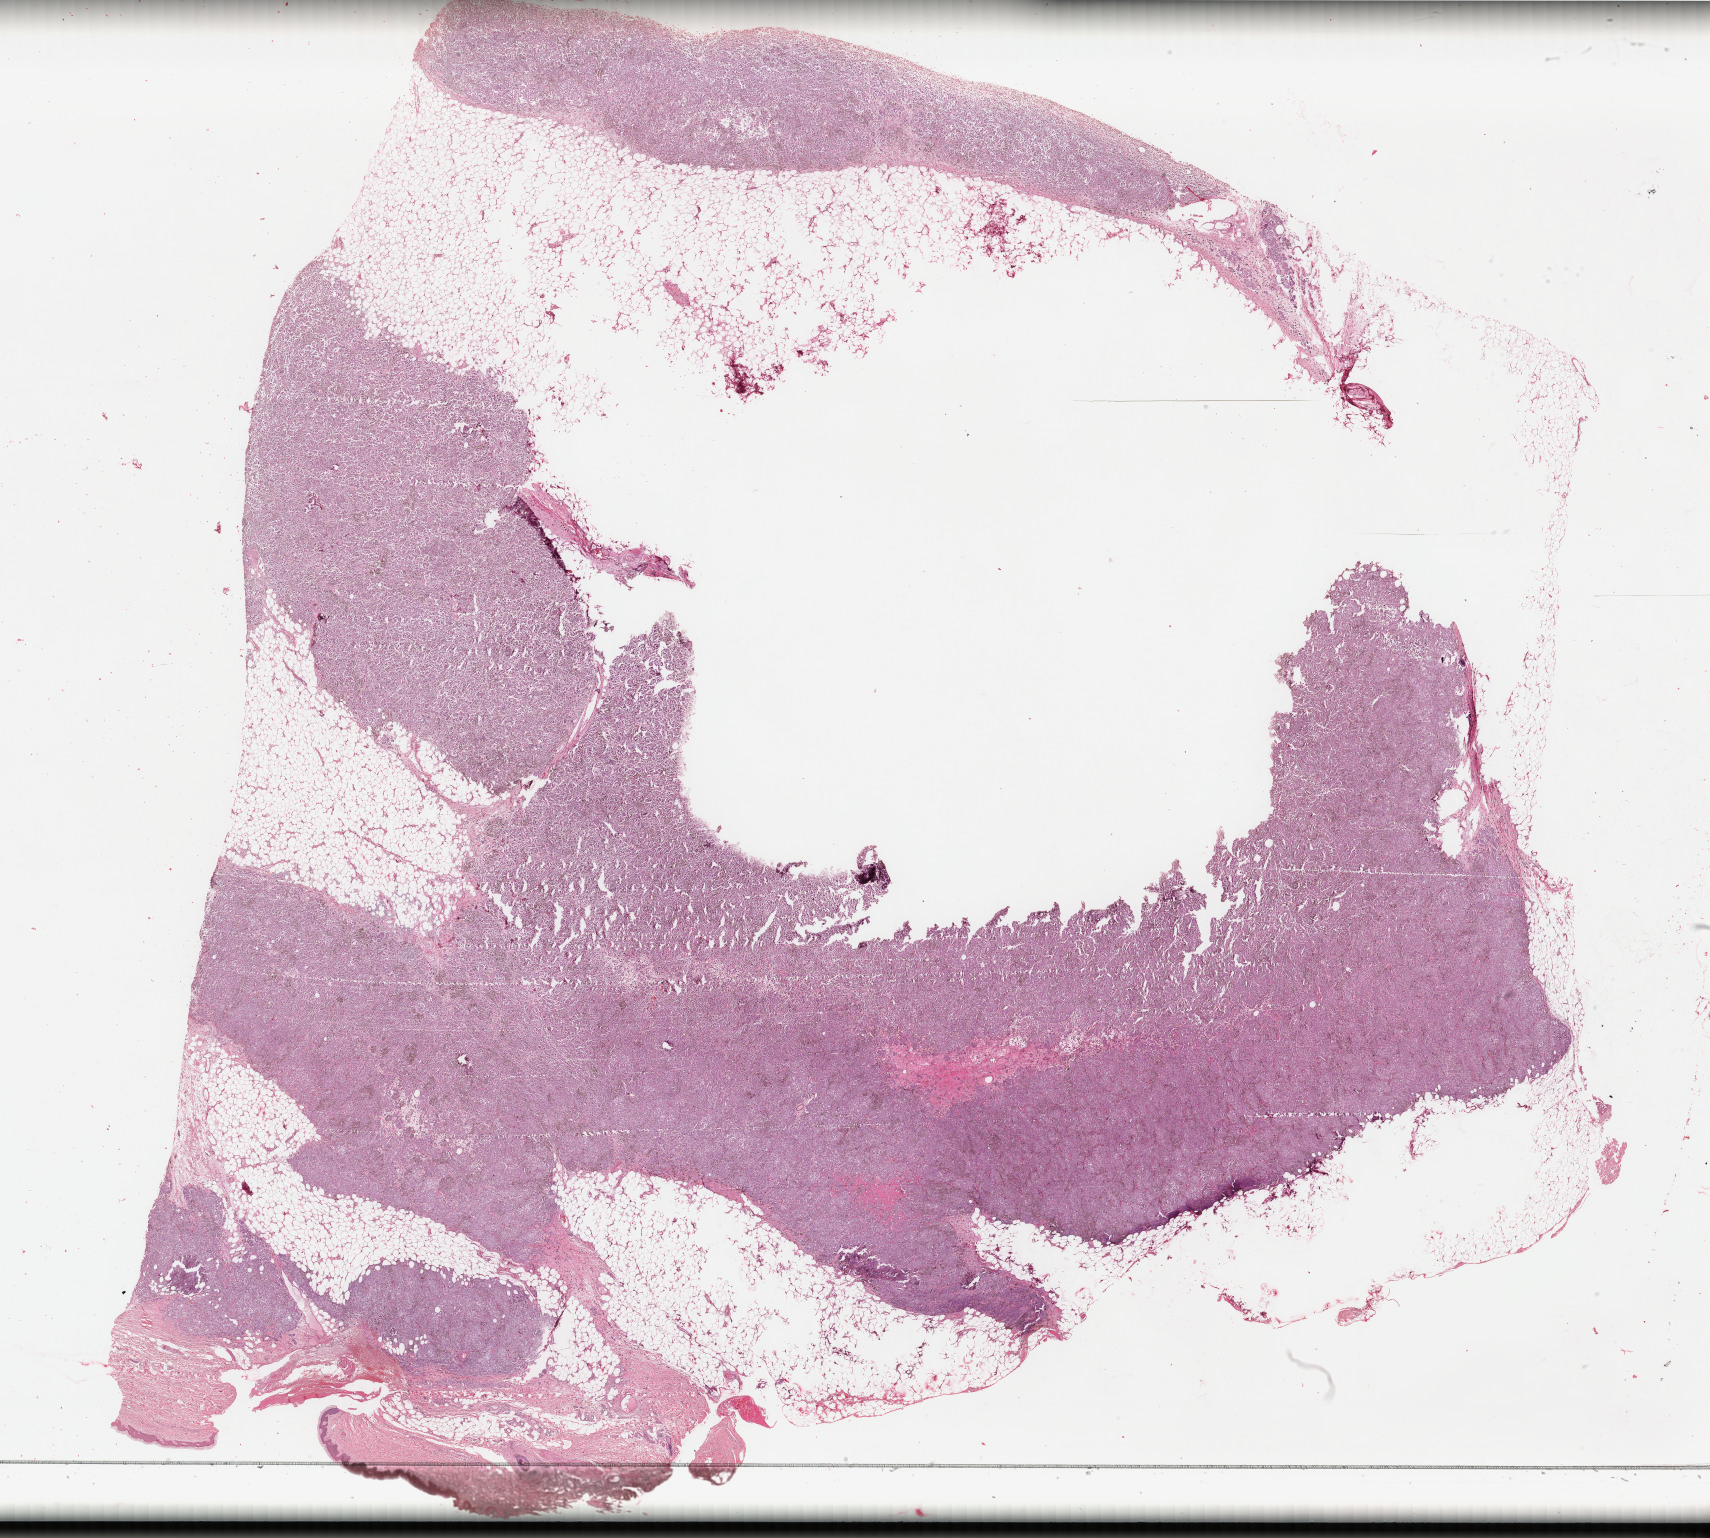
Digitized H&E-stained tissue section (whole slide), shown as a low-resolution overview of the whole scanned area (about 27.2 x 24.4 mm, from a 40x scan). FFPE section. Sample: primary tumour, skin. Patient: female, age at initial diagnosis 55 years.
- pathologic diagnosis: Malignant melanoma, NOS